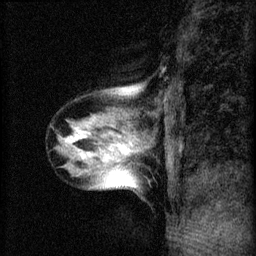
Breast MRI (dynamic contrast-enhanced), one sagittal slice; slice 19 of 60 in the series (ordered by position); 3 images stored at this slice position (order not interpretable as contrast timing); 1.5 T; TE 4.2 ms, TR 8.2 ms; 2 mm slice thickness; 256 × 256 image matrix. Patient: female, 40 years.
Structures marked on this image (semi-automatic segmentation, software-assisted and operator-edited):
- analysis volume of interest (the breast-tissue region the enhancement analysis was run in; not a lesion): bounding box [x1, y1, x2, y2] px = [55, 80, 166, 193]
- tumour enhancement mask (voxels above the 70 % enhancement threshold inside the analysis volume of interest): [71, 92, 133, 157]